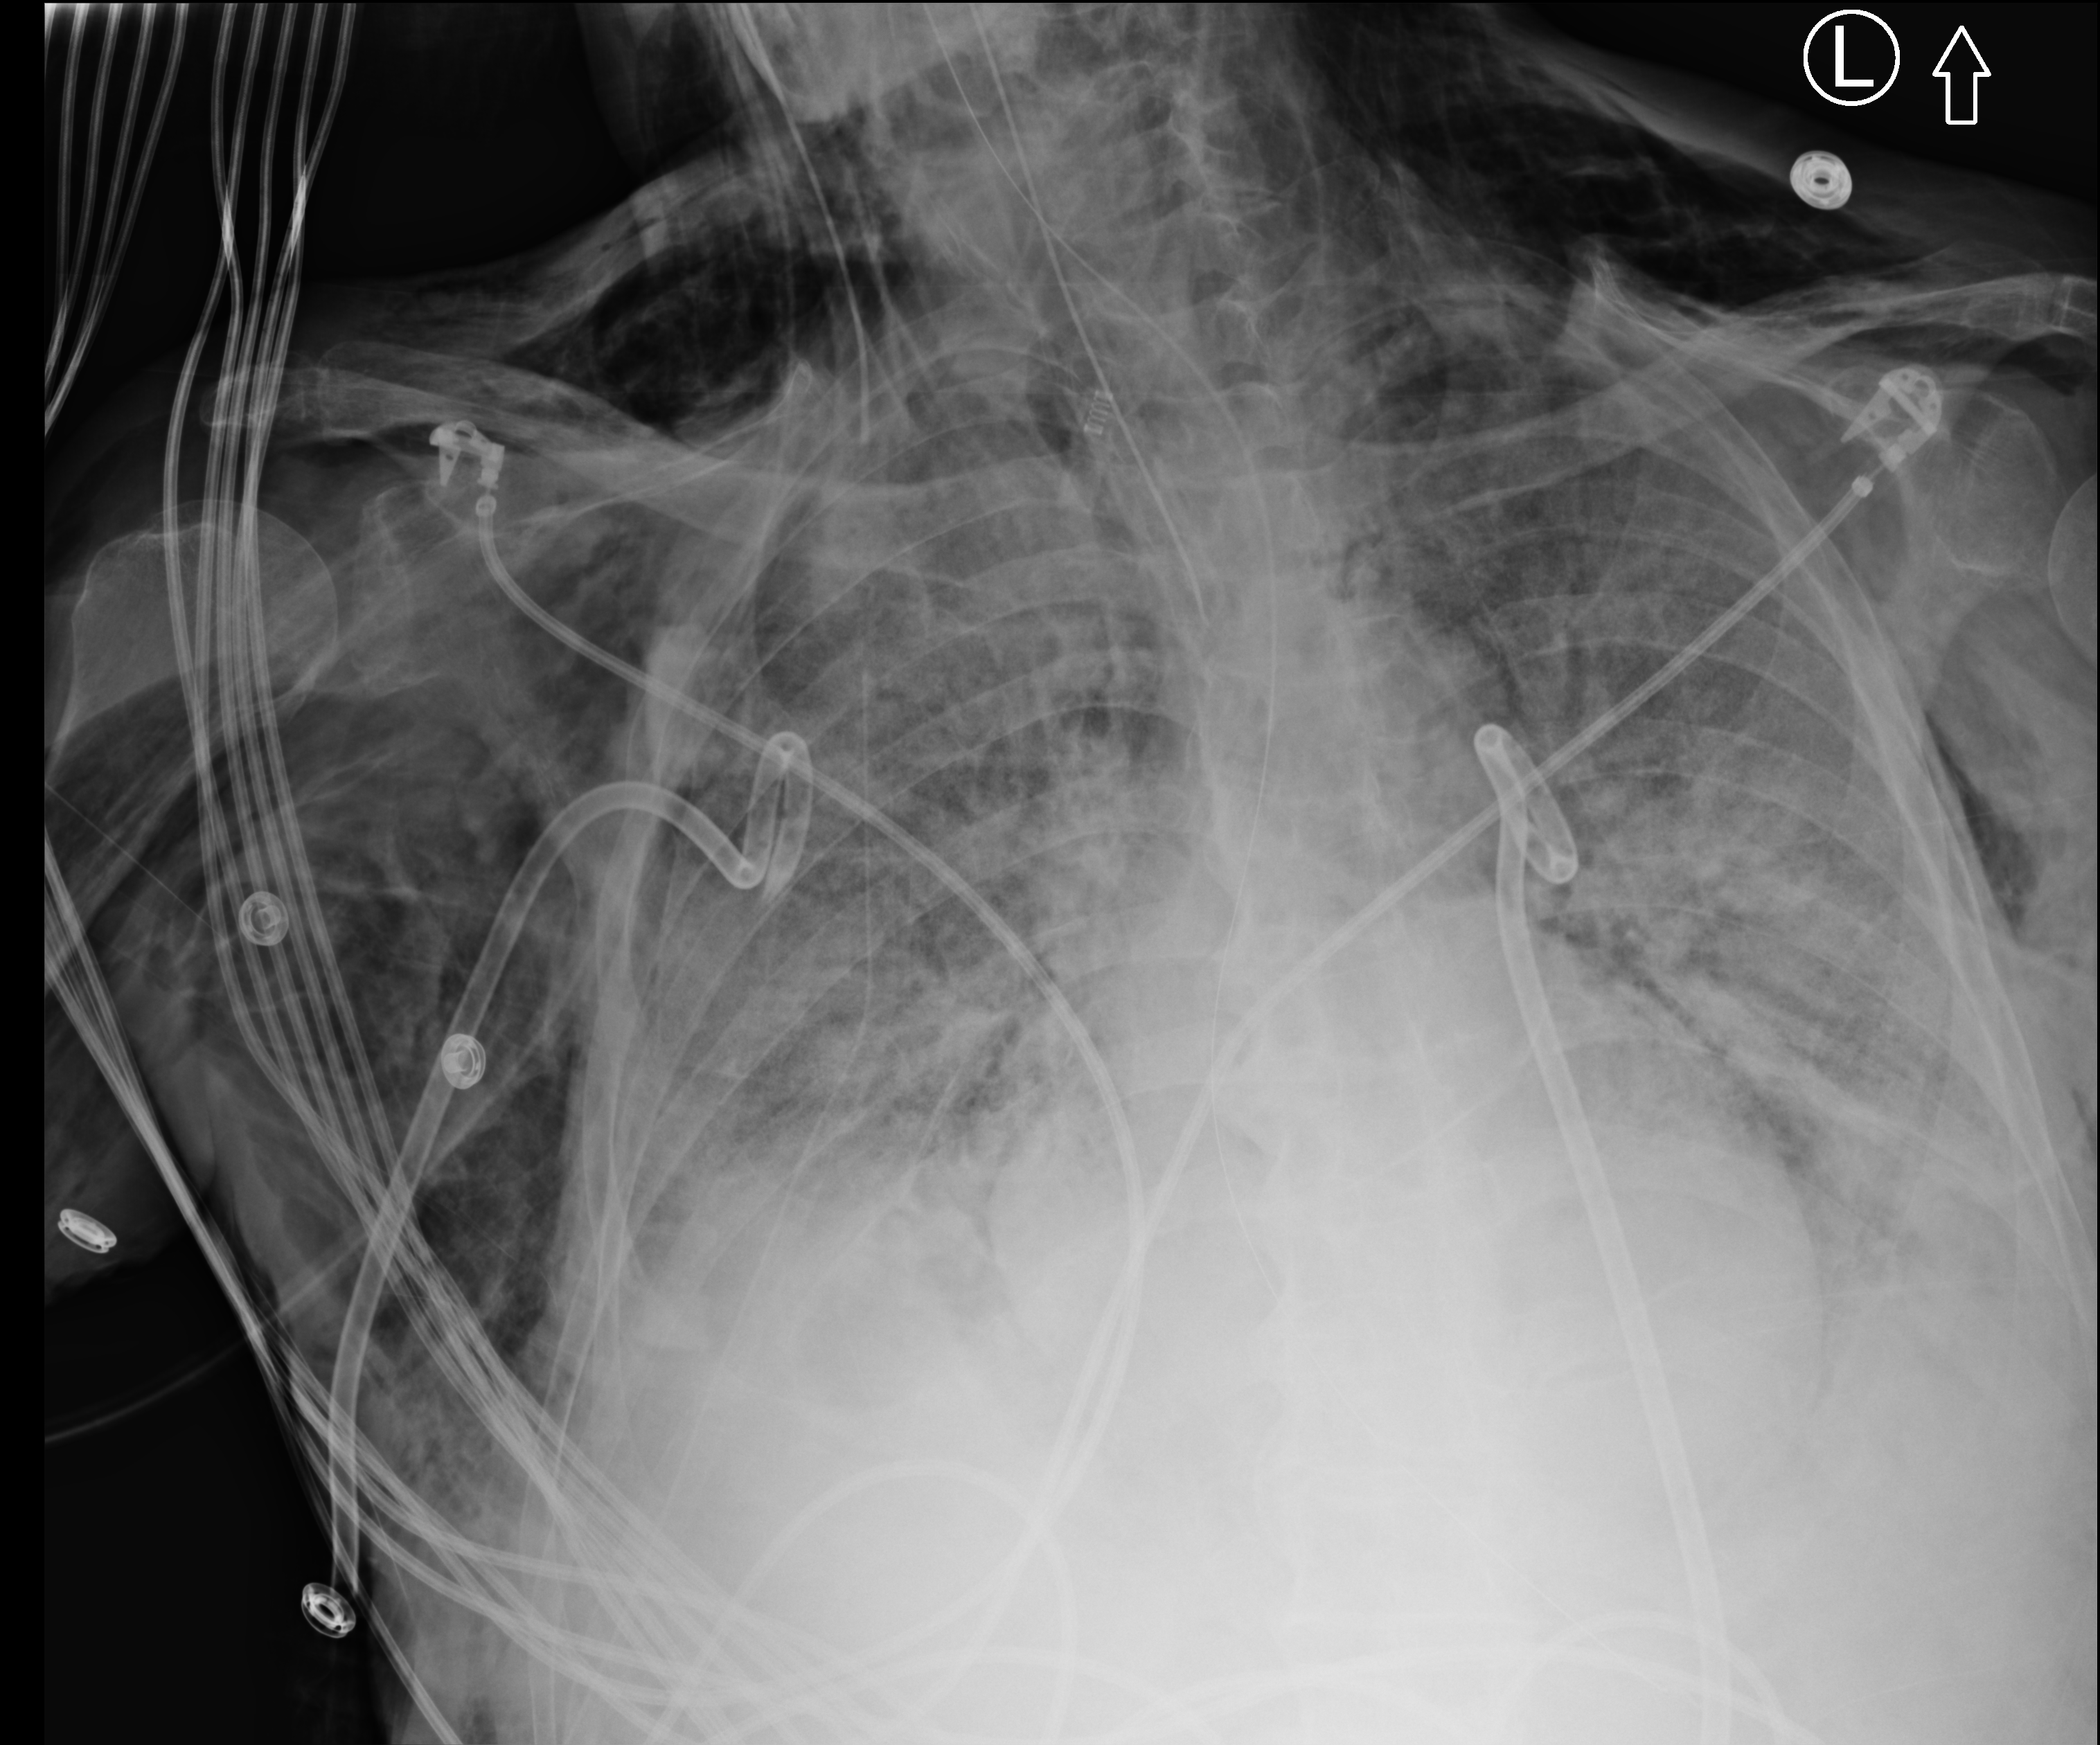
Portable chest radiograph; anteroposterior (AP) projection. Male patient hospitalised with COVID-19, age 75–90 years.
From the hospital-stay record, not from the radiograph (when in the stay this image was taken is not recorded):
- mechanically ventilated during this hospital stay: yes
- COPD (admission record): no
- admitted to intensive care during this hospital stay: yes